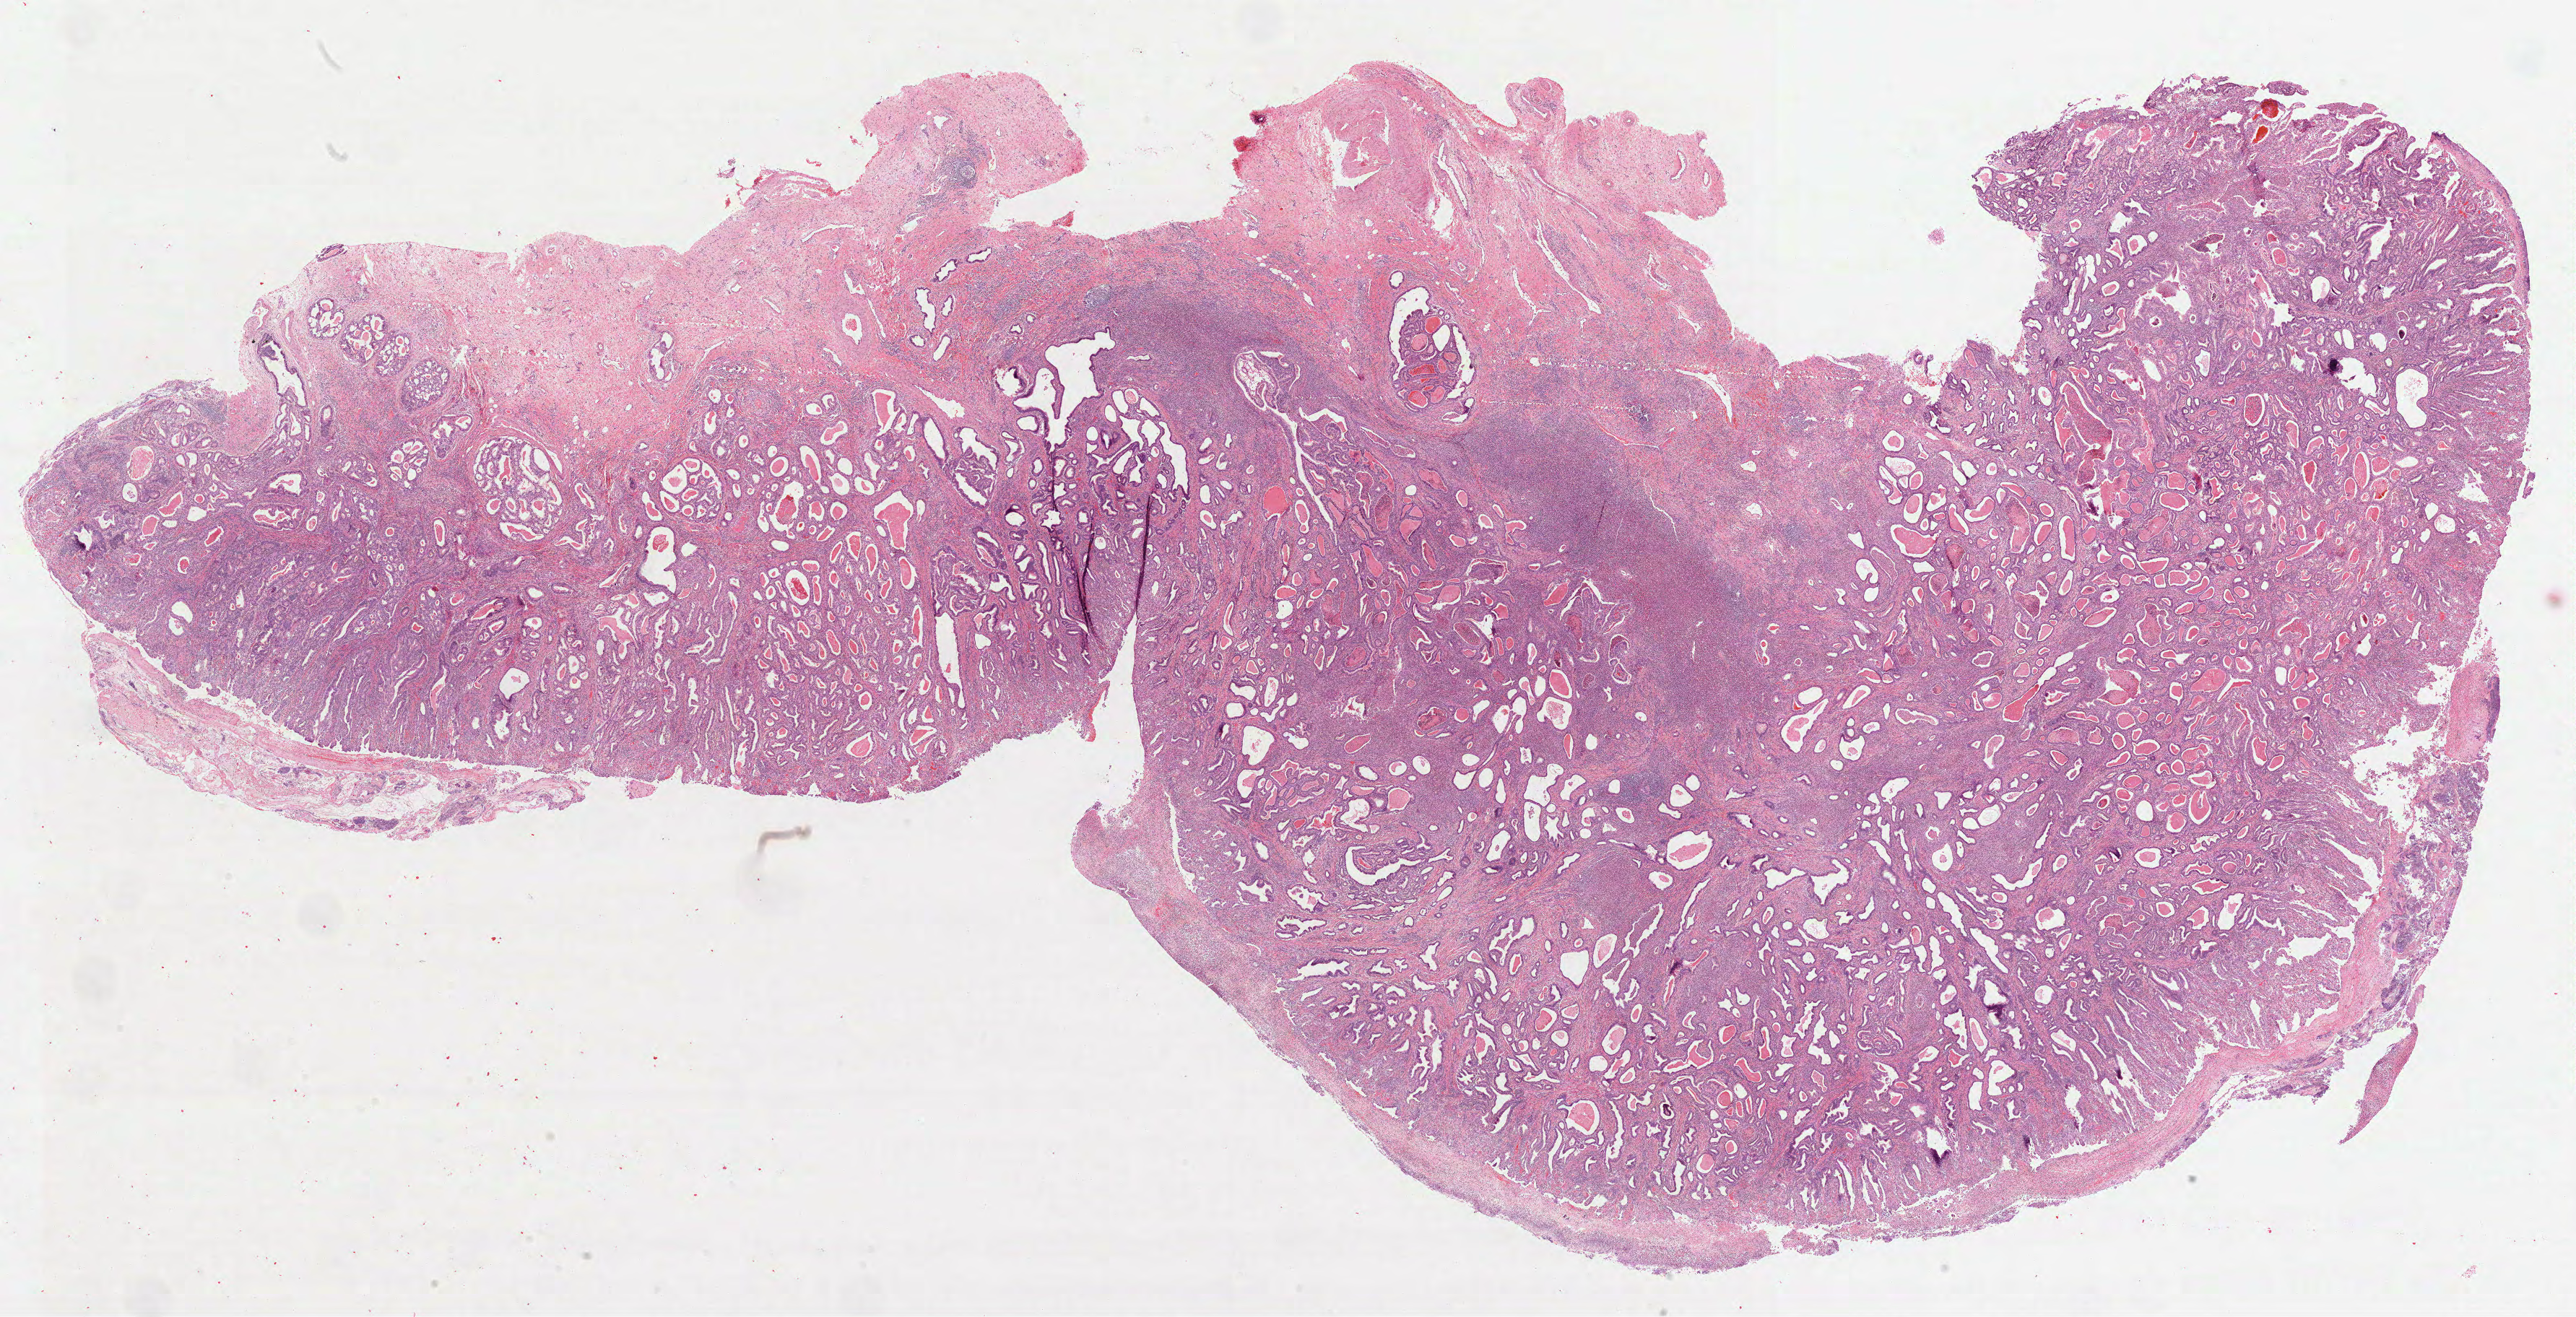
Whole-slide histology image, Hematoxylin and eosin (H&E) stained, shown as a low-resolution overview of the whole scanned area (about 28.8 x 14.7 mm). Formalin-fixed paraffin-embedded (FFPE) diagnostic section. Sample: primary tumour, stomach. Female patient.
Diagnosis: Adenocarcinoma, NOS (fundus of stomach).